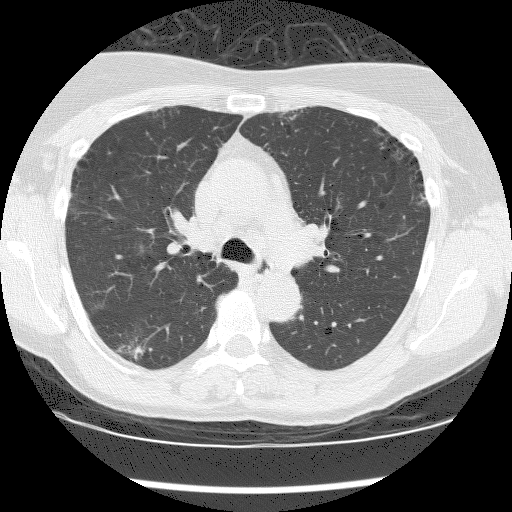
Low-dose screening chest CT, one axial slice. Slice 122 of 176 in the series (ordered by position). Reconstruction kernel BONE. 120 kVp. Lung window (W 1500 / L -600 HU). 512 × 512 image matrix, field of view 320 × 320 mm.
Outlined on this slice (manually delineated by an expert):
- lesion 1 (tumor, lower lobe of right lung): bounding box [x1, y1, x2, y2] px = [118, 345, 145, 360]